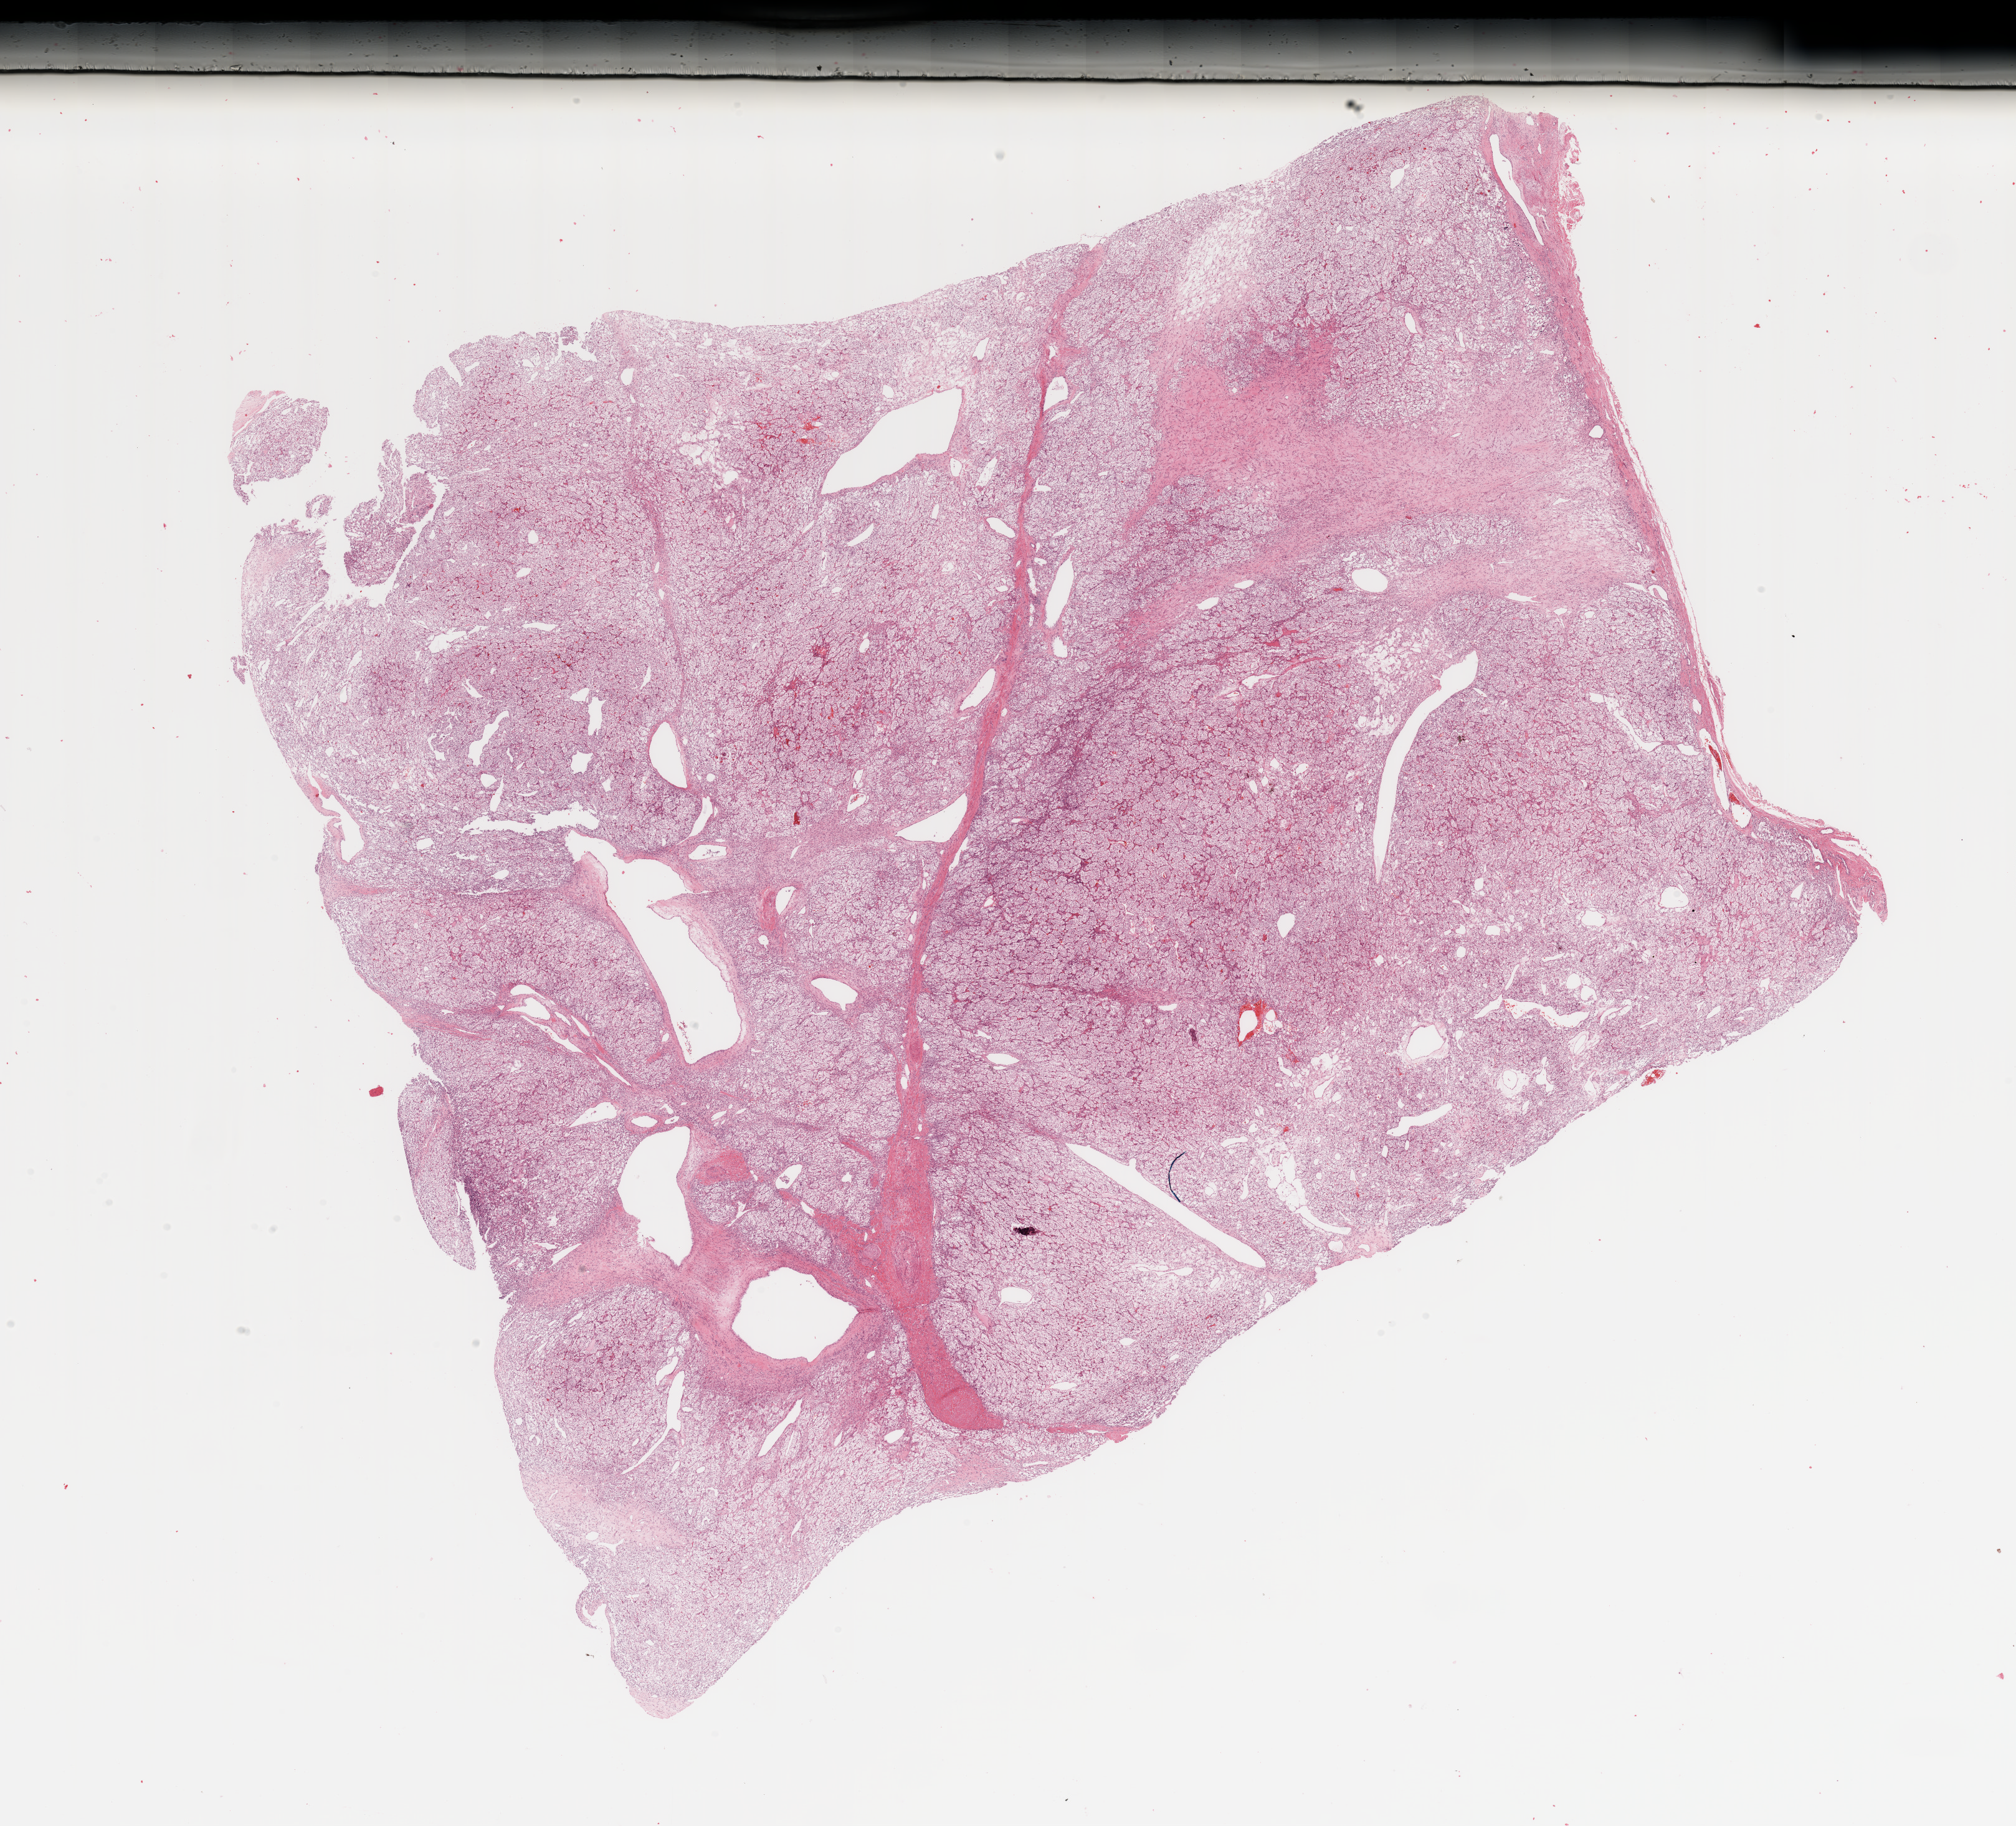
H&E-stained whole-slide image, whole scanned area (about 25.6 x 23.2 mm) shown as a low-resolution overview, tumour tissue sample, sampled site: kidney. 57-year-old female patient. Histologic grade: G1 (well differentiated). Composition of this section per pathologist review: tumour nuclei 85%, necrosis 5%.
Diagnosis: Renal cell carcinoma, NOS.